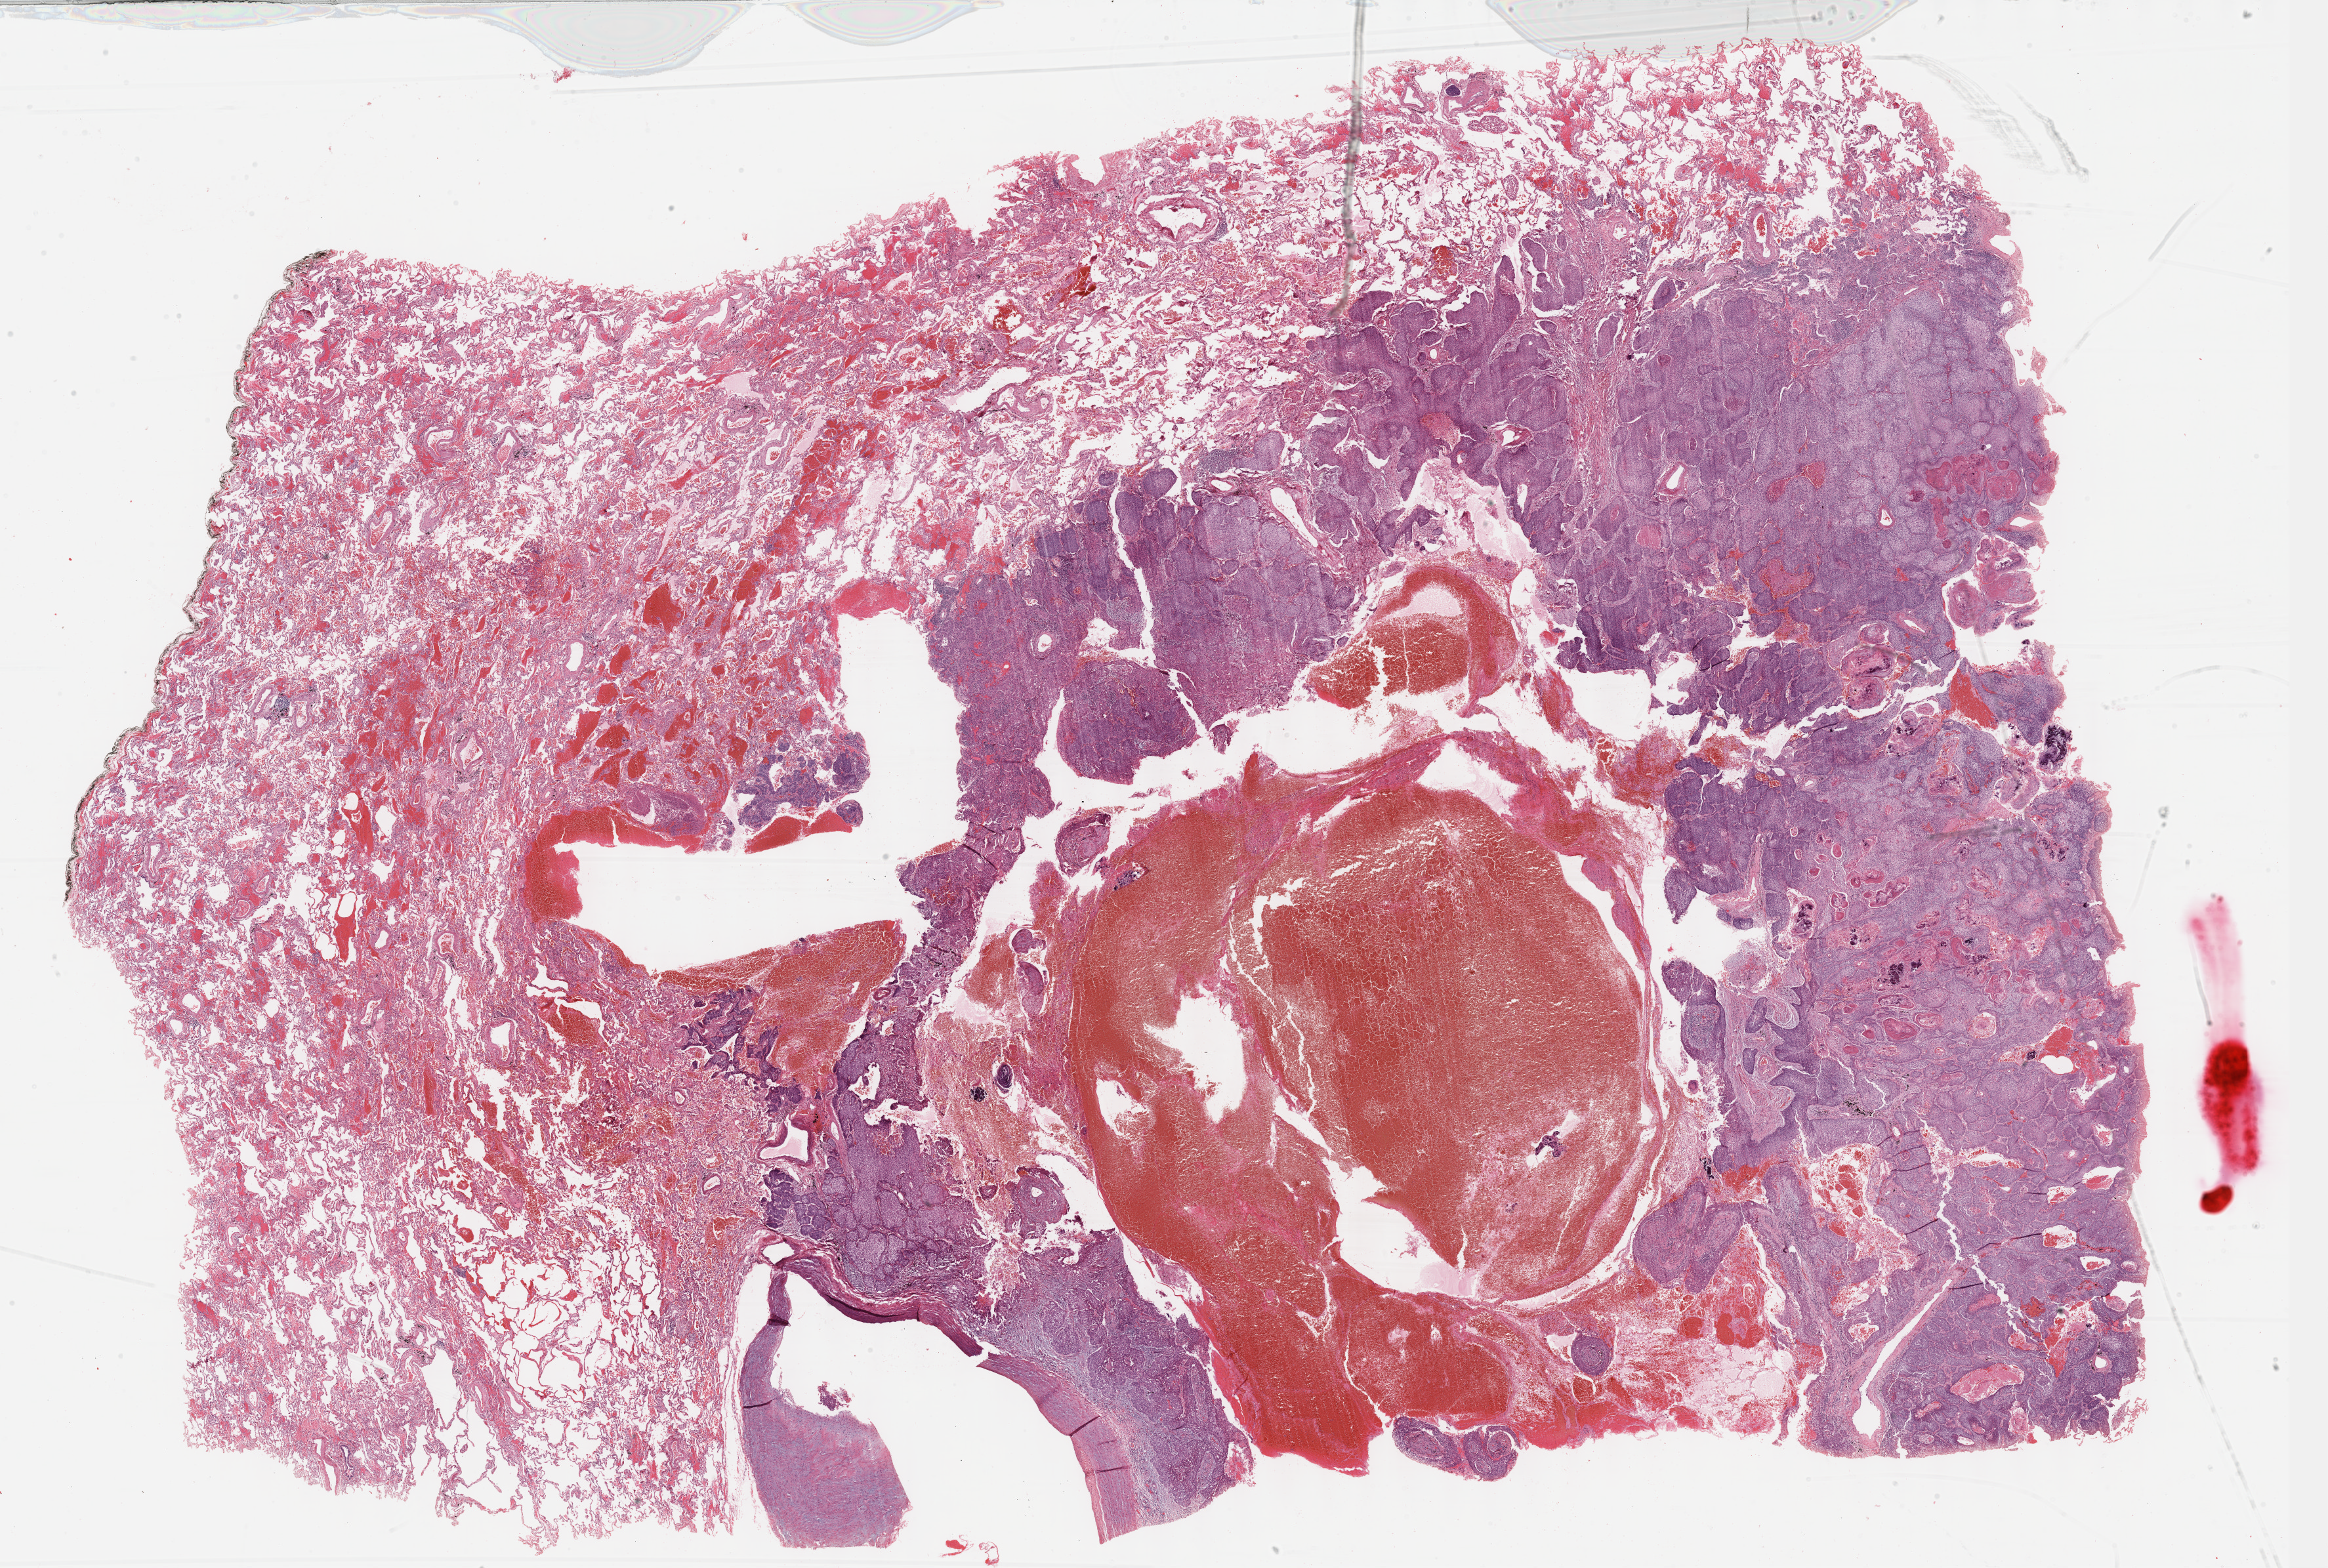
Whole-slide histology image, H&E-stained — a low-resolution overview of the entire scanned area, about 28.7 x 19.3 mm (slide scanned at 40x), formalin-fixed paraffin-embedded (FFPE) diagnostic section, lung, primary tumour sample. Female, age 76 years at initial diagnosis.
AJCC pathologic stage: IA. Histologic diagnosis: Squamous cell carcinoma, NOS (lower lobe, lung).